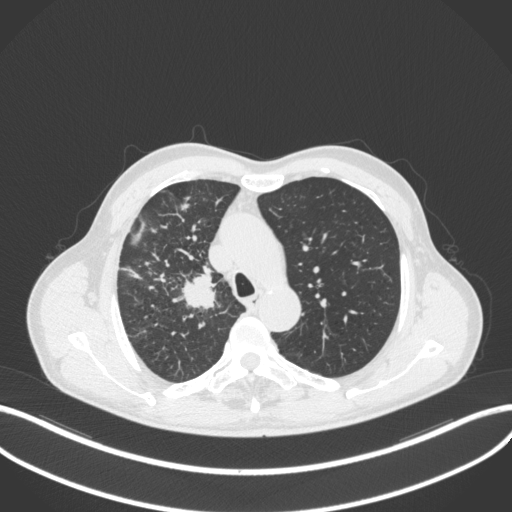
Chest CT, one axial slice. Slice 351 of 490 in the series (ordered by position). Reconstruction kernel B31f. 120 kVp. Lung window (W 1500 / L -600 HU). 1 mm slice thickness. 512 × 512 image matrix, field of view 400 × 400 mm. Male patient, age 69 years. Case-level facts recorded for this patient, not image findings: clinical TNM (as recorded): T2a N0 M0.
Outlined on this slice (rectangle marked by the reading radiologist):
- lung tumour (recorded histology: adenocarcinoma): bounding box <178,268,226,313> (left, top, right, bottom; pixels)